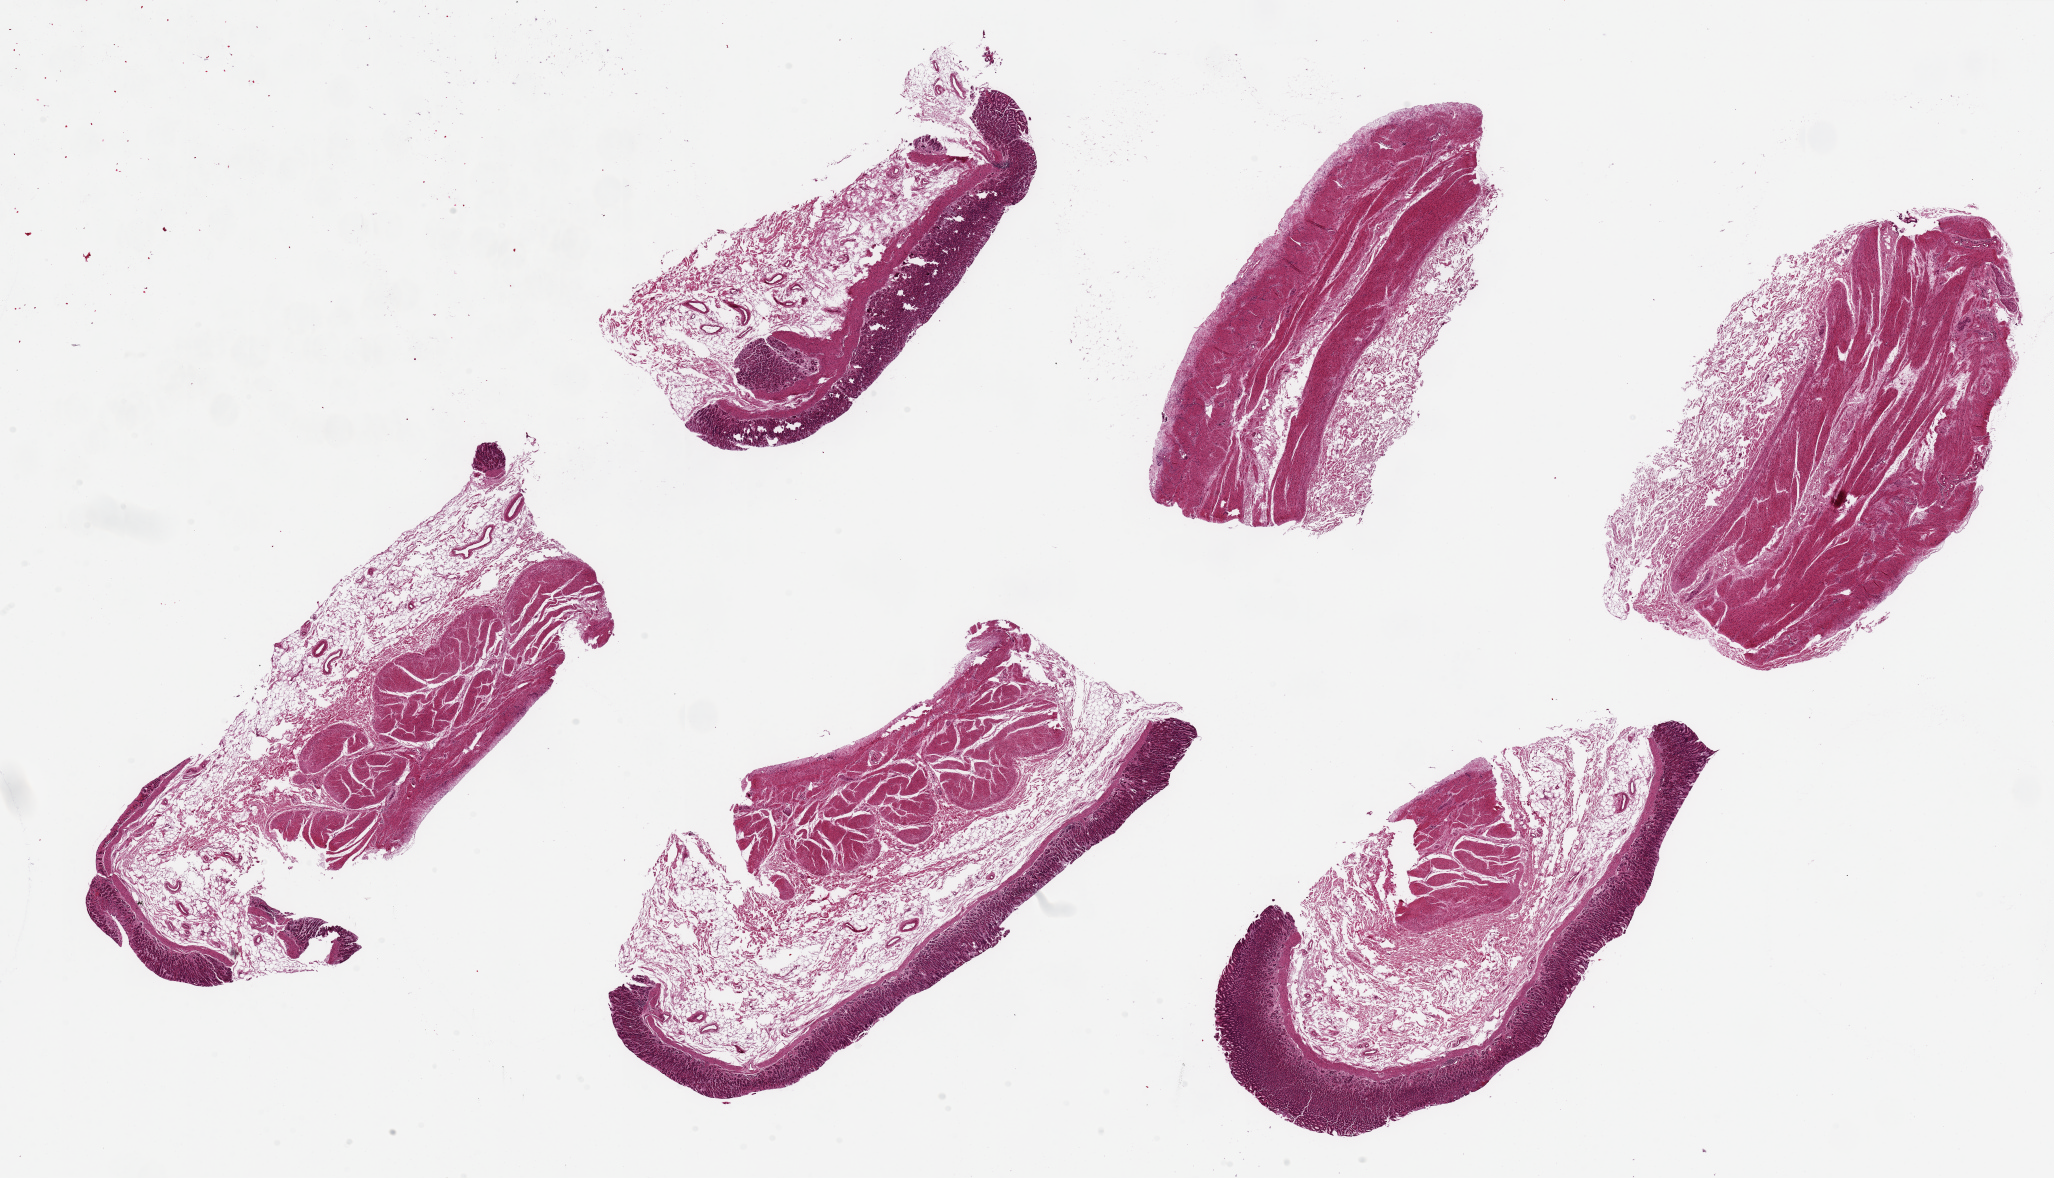
Whole-slide image, H&E stain, a low-resolution overview of the entire scanned area, about 32.5 x 18.6 mm (acquisition: 20x scan); PAXgene-fixed paraffin-embedded (PFPE) section; sampled site (target tissue): stomach; donor tissue sample. Donor: female.
Review note (as recorded): 6 pieces up to 9x4 mm; 4 have well preserved oxyntic mucosa, 2 have only muscularis.